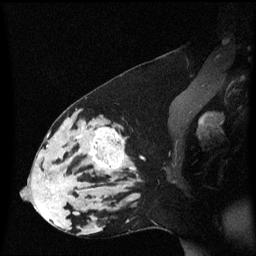
Breast MRI (dynamic contrast-enhanced), one sagittal slice; slice 32 of 60 in the series (ordered by position); dynamic contrast-enhanced series, image 2 of 3 at this slice position (ordered by acquisition); 1.5 T; TE 4.2 ms, TR 8.4 ms; 2 mm slice thickness; 256 × 256 image matrix. Female patient, age 33 years. Case-level facts recorded for this patient, not image findings: setting: breast cancer imaged before/during neoadjuvant chemotherapy; receptor status: triple-negative.
Structures marked on this image (semi-automatic segmentation, software-assisted and operator-edited):
- analysis volume of interest (the breast-tissue region the enhancement analysis was run in; not a lesion): box from (x=44, y=123) to (x=138, y=189) px
- tumour enhancement mask (voxels above the 70 % enhancement threshold inside the analysis volume of interest): (x=45, y=128)–(x=125, y=173)